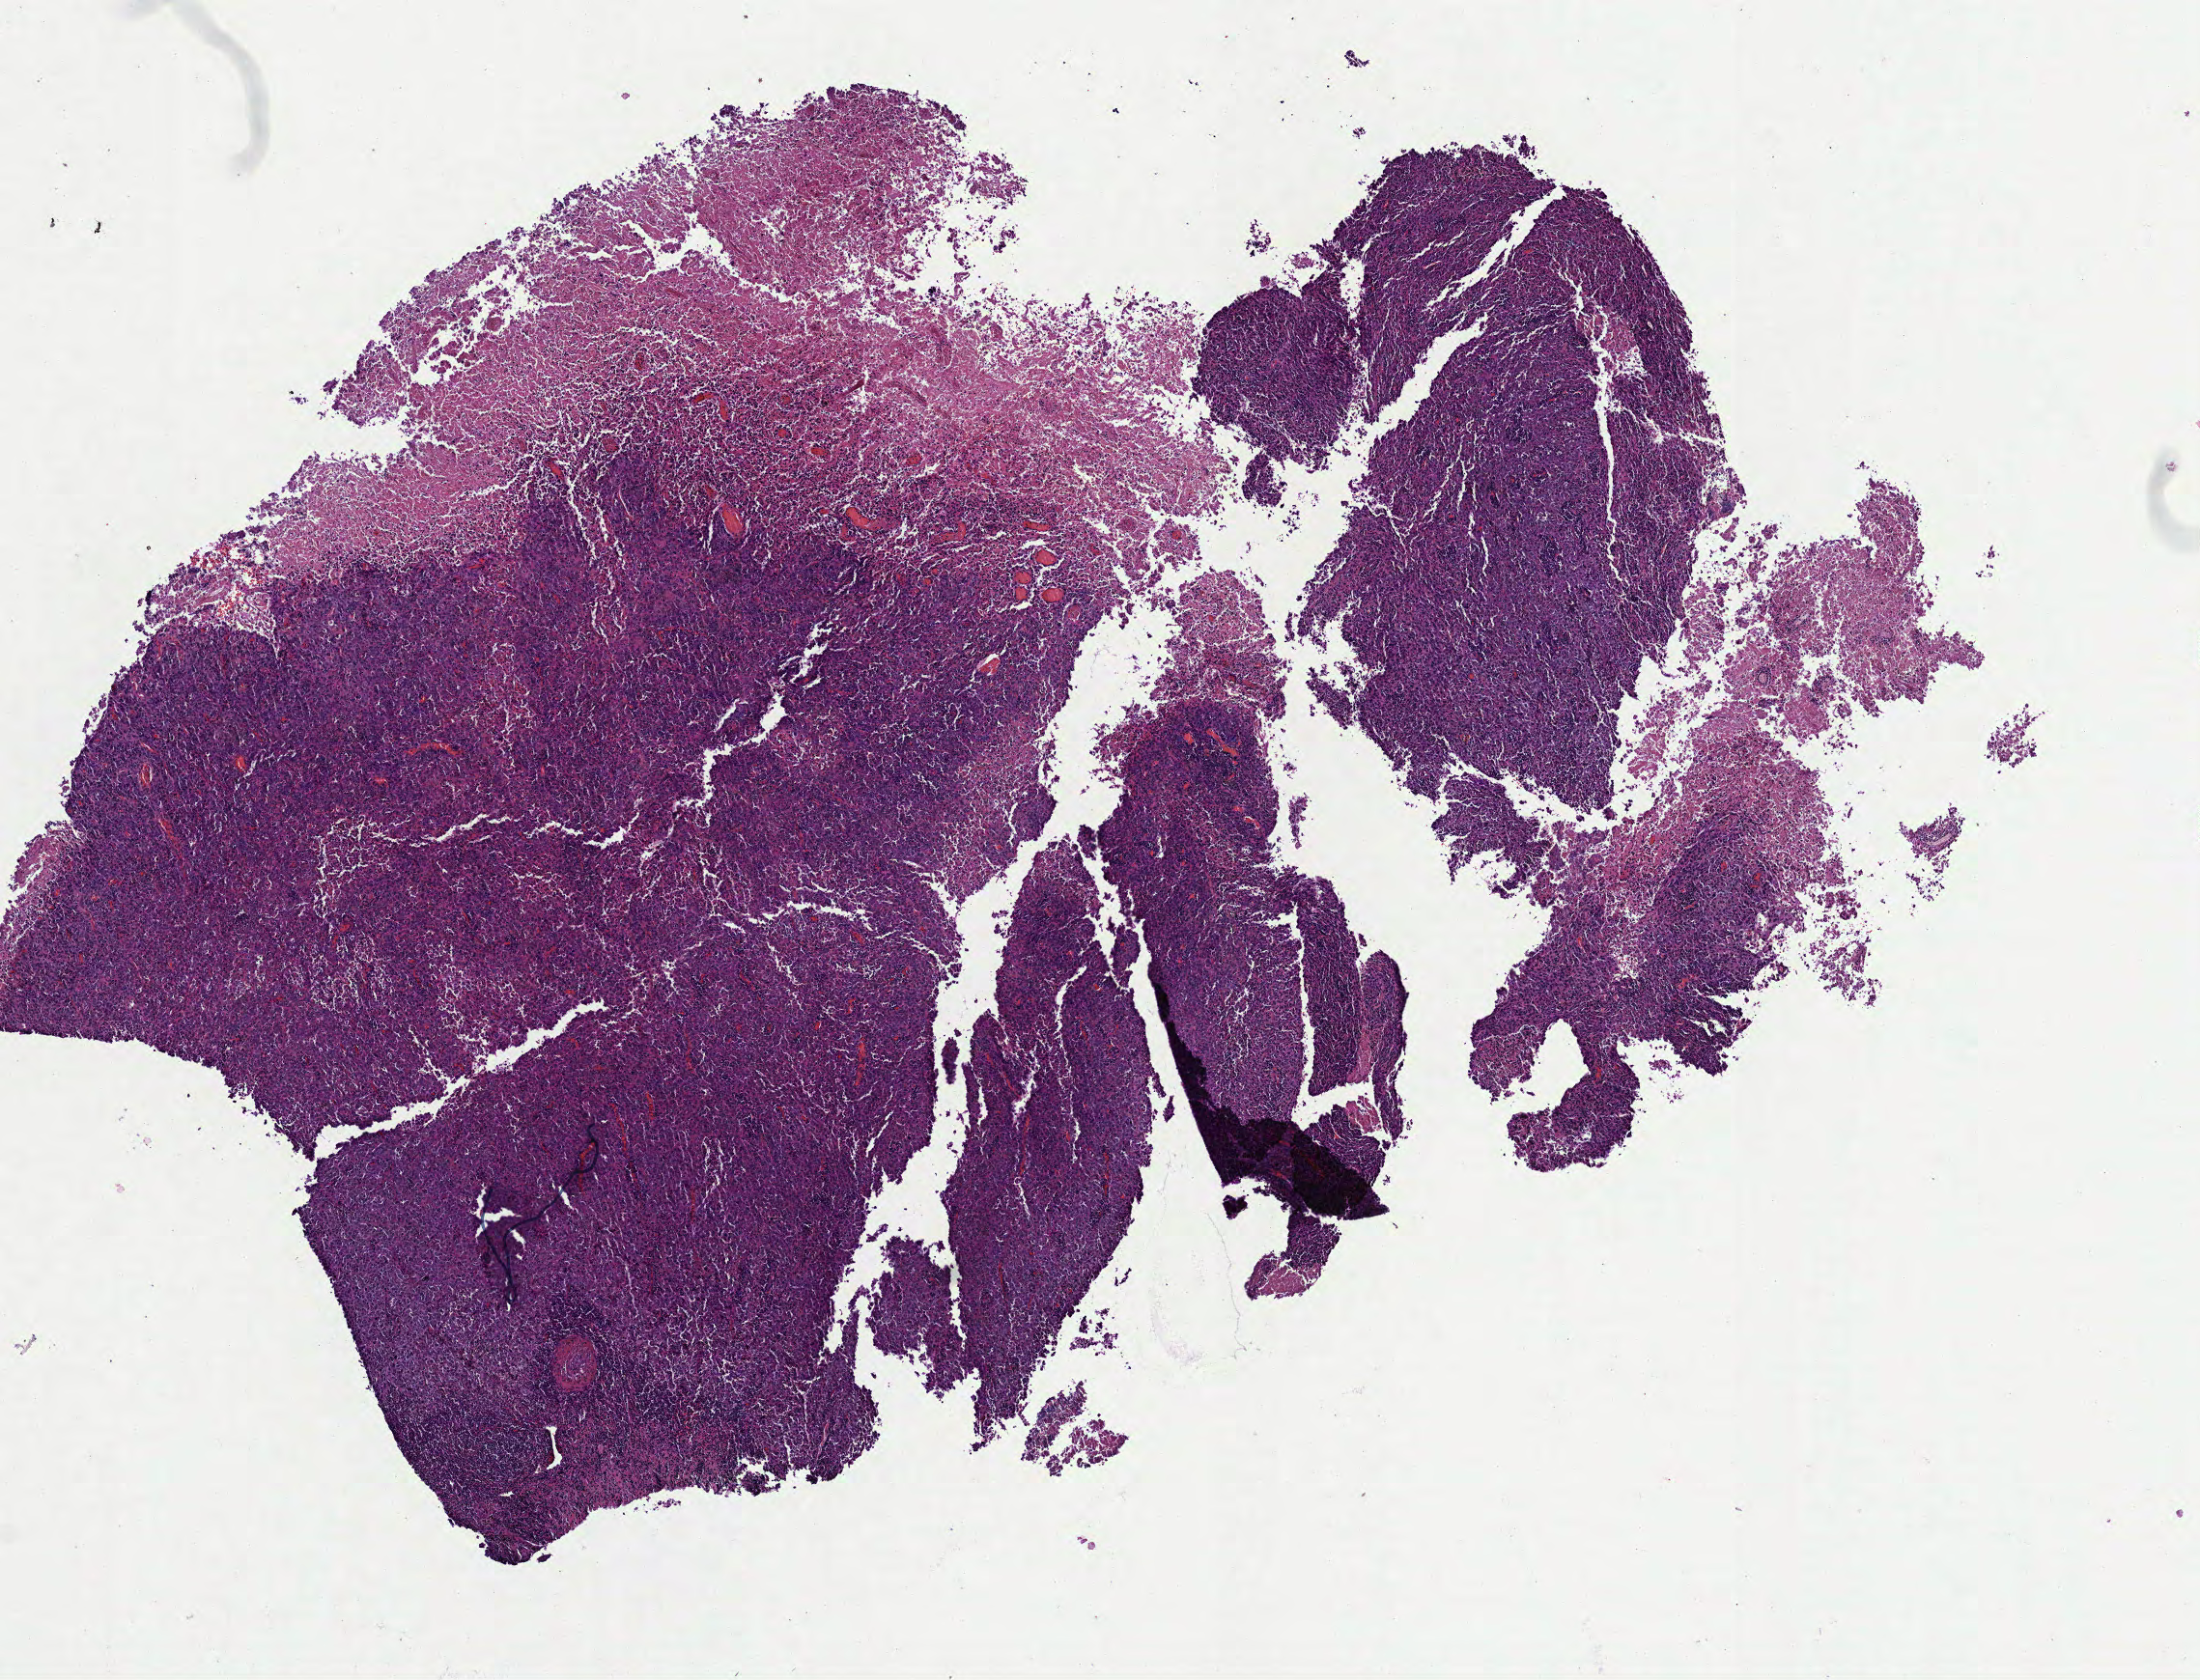
Digitized H&E-stained tissue section (whole slide) — shown as a low-resolution overview of the whole scanned area (about 9.2 x 7.0 mm); FFPE section; bladder, primary tumour sample. Female patient. Histologic grade: high grade.
• histologic diagnosis: Transitional cell carcinoma
• lymph nodes positive (case pathology): 0 of 8 examined
• AJCC pathologic stage: II (7th edition)